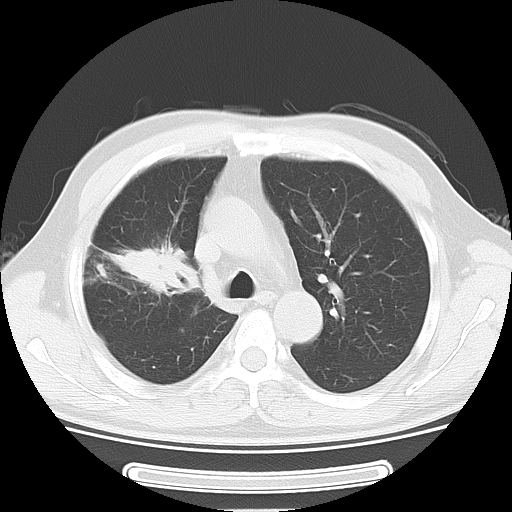
Chest CT, one axial slice; position 36 of 51 along the scan axis; lung window (W 1500 / L -600 HU); 5 mm slice thickness; 512 × 512 image matrix, field of view 350 × 350 mm. Male patient, age 46 years. From the clinical record (not read from this slice): clinical TNM (as recorded): T3 N0 M1b.
Annotated regions visible in this slice (rectangle marked by the reading radiologist):
- lung tumour (recorded histology: adenocarcinoma): bounding box [x1, y1, x2, y2] px = [105, 233, 189, 304]